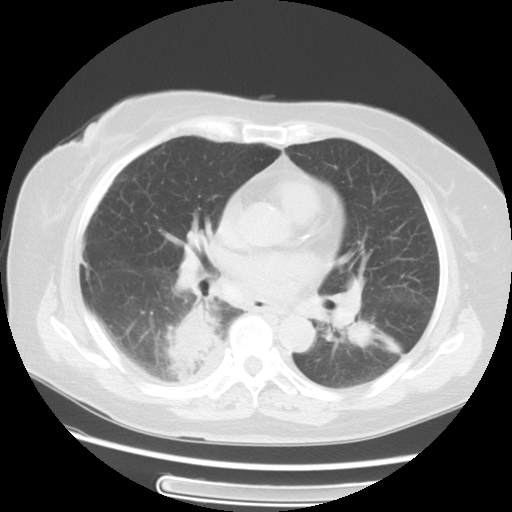
Chest CT, one axial slice; slice 31 of 57 in the series (ordered by position); 120 kVp; lung window (W 1500 / L -600 HU); 5 mm slice thickness; 512 × 512 image matrix, field of view 350 × 350 mm. Patient: female, 69 years. Case-level facts recorded for this patient, not image findings: clinical TNM (as recorded): T2 N1 M1a.
Outlined on this slice (bounding box drawn by a radiologist):
- lung tumour (recorded histology: adenocarcinoma): box from (x=158, y=298) to (x=219, y=386) px